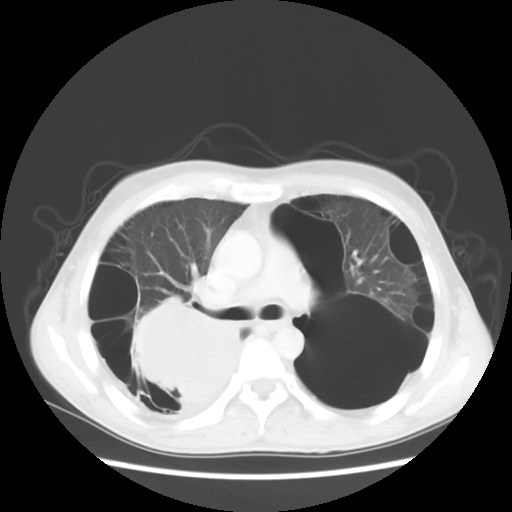
Chest CT, one axial slice; slice 34 of 56 in the series (ordered by position); reconstruction kernel STANDARD; 140 kVp; lung window (W 1500 / L -600 HU); 5 mm slice thickness; 512 × 512 image matrix, field of view 351 × 351 mm. Patient: male, 41 years. From the clinical record (not read from this slice): clinical TNM (as recorded): T4 N0 M1a; histopathological grade: G3.
Annotated regions visible in this slice (bounding box drawn by a radiologist):
- lung tumour (recorded histology: large cell carcinoma): bounding box [x1, y1, x2, y2] px = [120, 290, 242, 400]